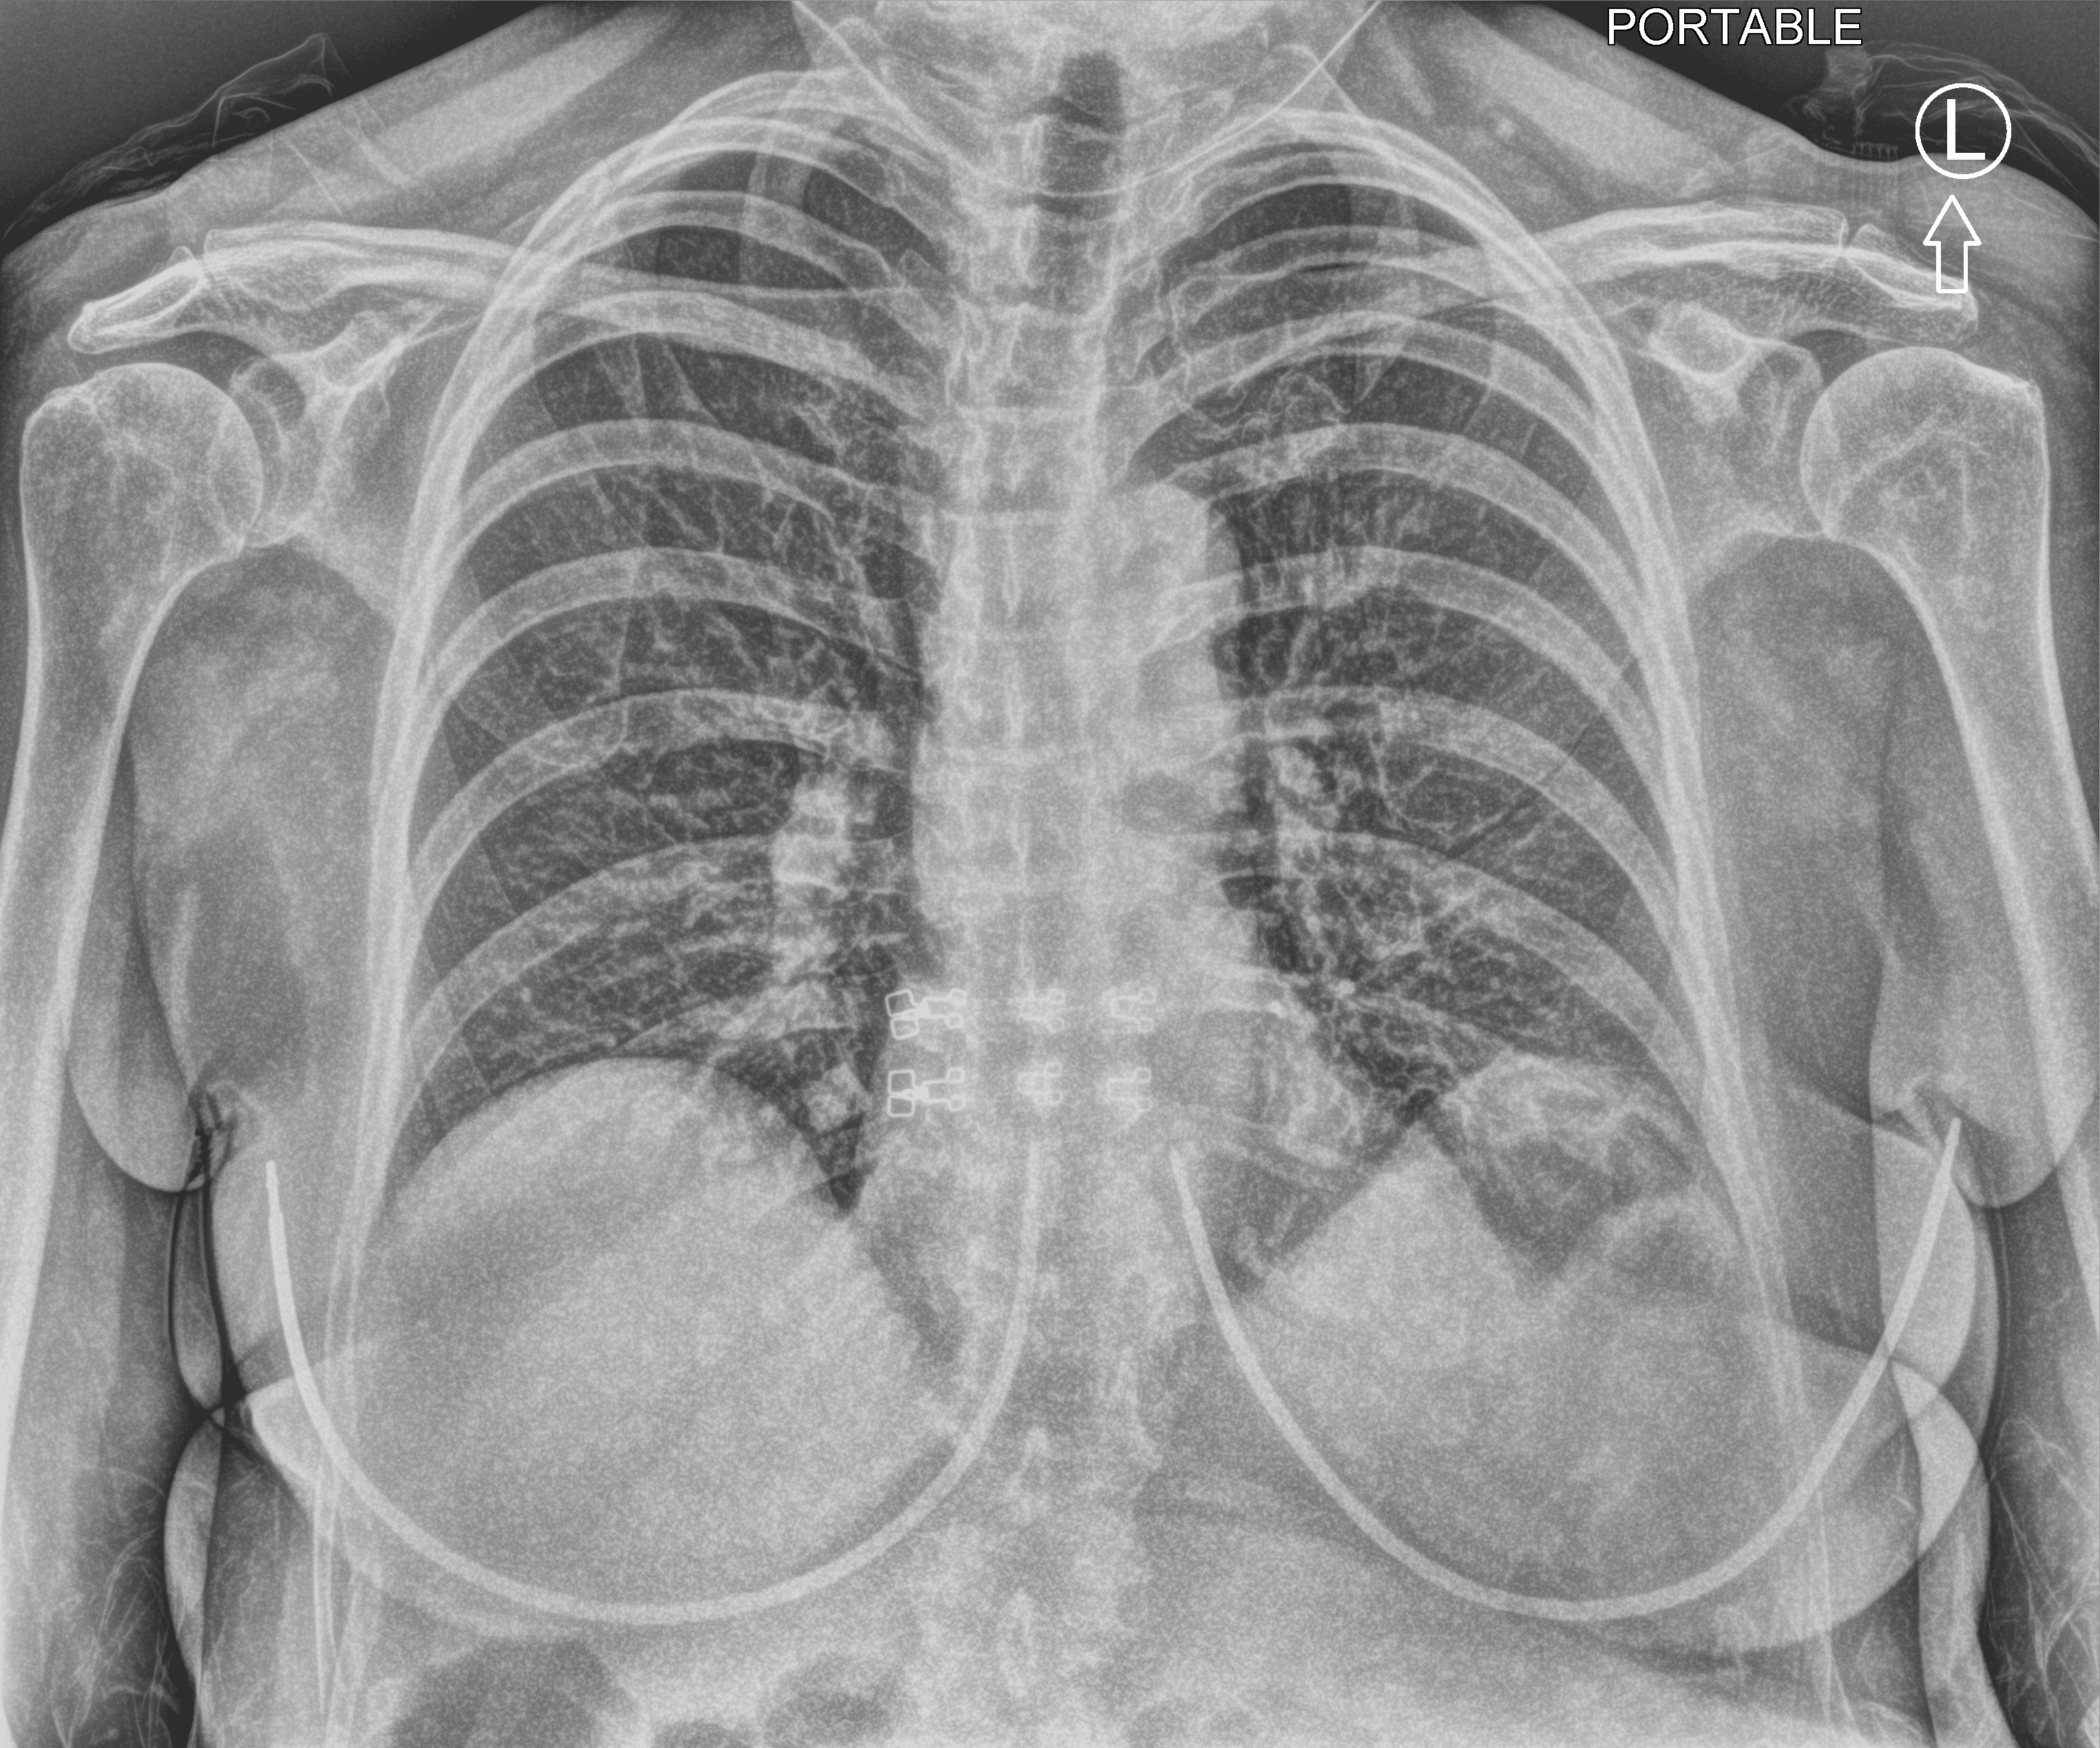
Bedside chest radiograph (computed radiography); anteroposterior (AP) projection. Female patient hospitalised with COVID-19, age 75–90 years.
Hospital-stay facts (about this admission, not read from this image; timing relative to this image not recorded): admitted to intensive care during this hospital stay: no.